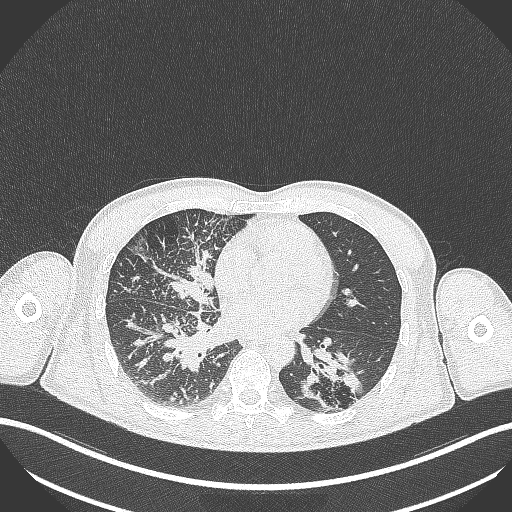
Chest CT, one axial slice. Position 137 of 348 along the scan axis. Reconstruction kernel B70f. 120 kVp. Lung window (W 1500 / L -600 HU). 1 mm slice thickness. 512 × 512 image matrix. Patient: male, 49 years. Case-level facts recorded for this patient, not image findings: clinical TNM (as recorded): T2b N1 M0.
Structures marked on this image (bounding box drawn by a radiologist):
- lung tumour (recorded histology: adenocarcinoma): bounding box (x1, y1, x2, y2) in pixels: (289, 338, 369, 411)